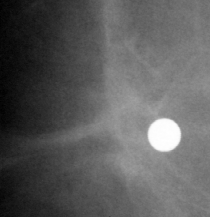
Cropped region of a digitized screen-film mammogram centred on a radiologist-marked abnormality; right breast; CC view; BI-RADS breast density category 1 (scale 1–4).
Marked abnormality: mass, shape irregular, margins ill defined; BI-RADS assessment category 1; subtlety rating 1 on a 1 (subtle) to 5 (obvious) scale; pathology result (as recorded, not read from the image): malignant.